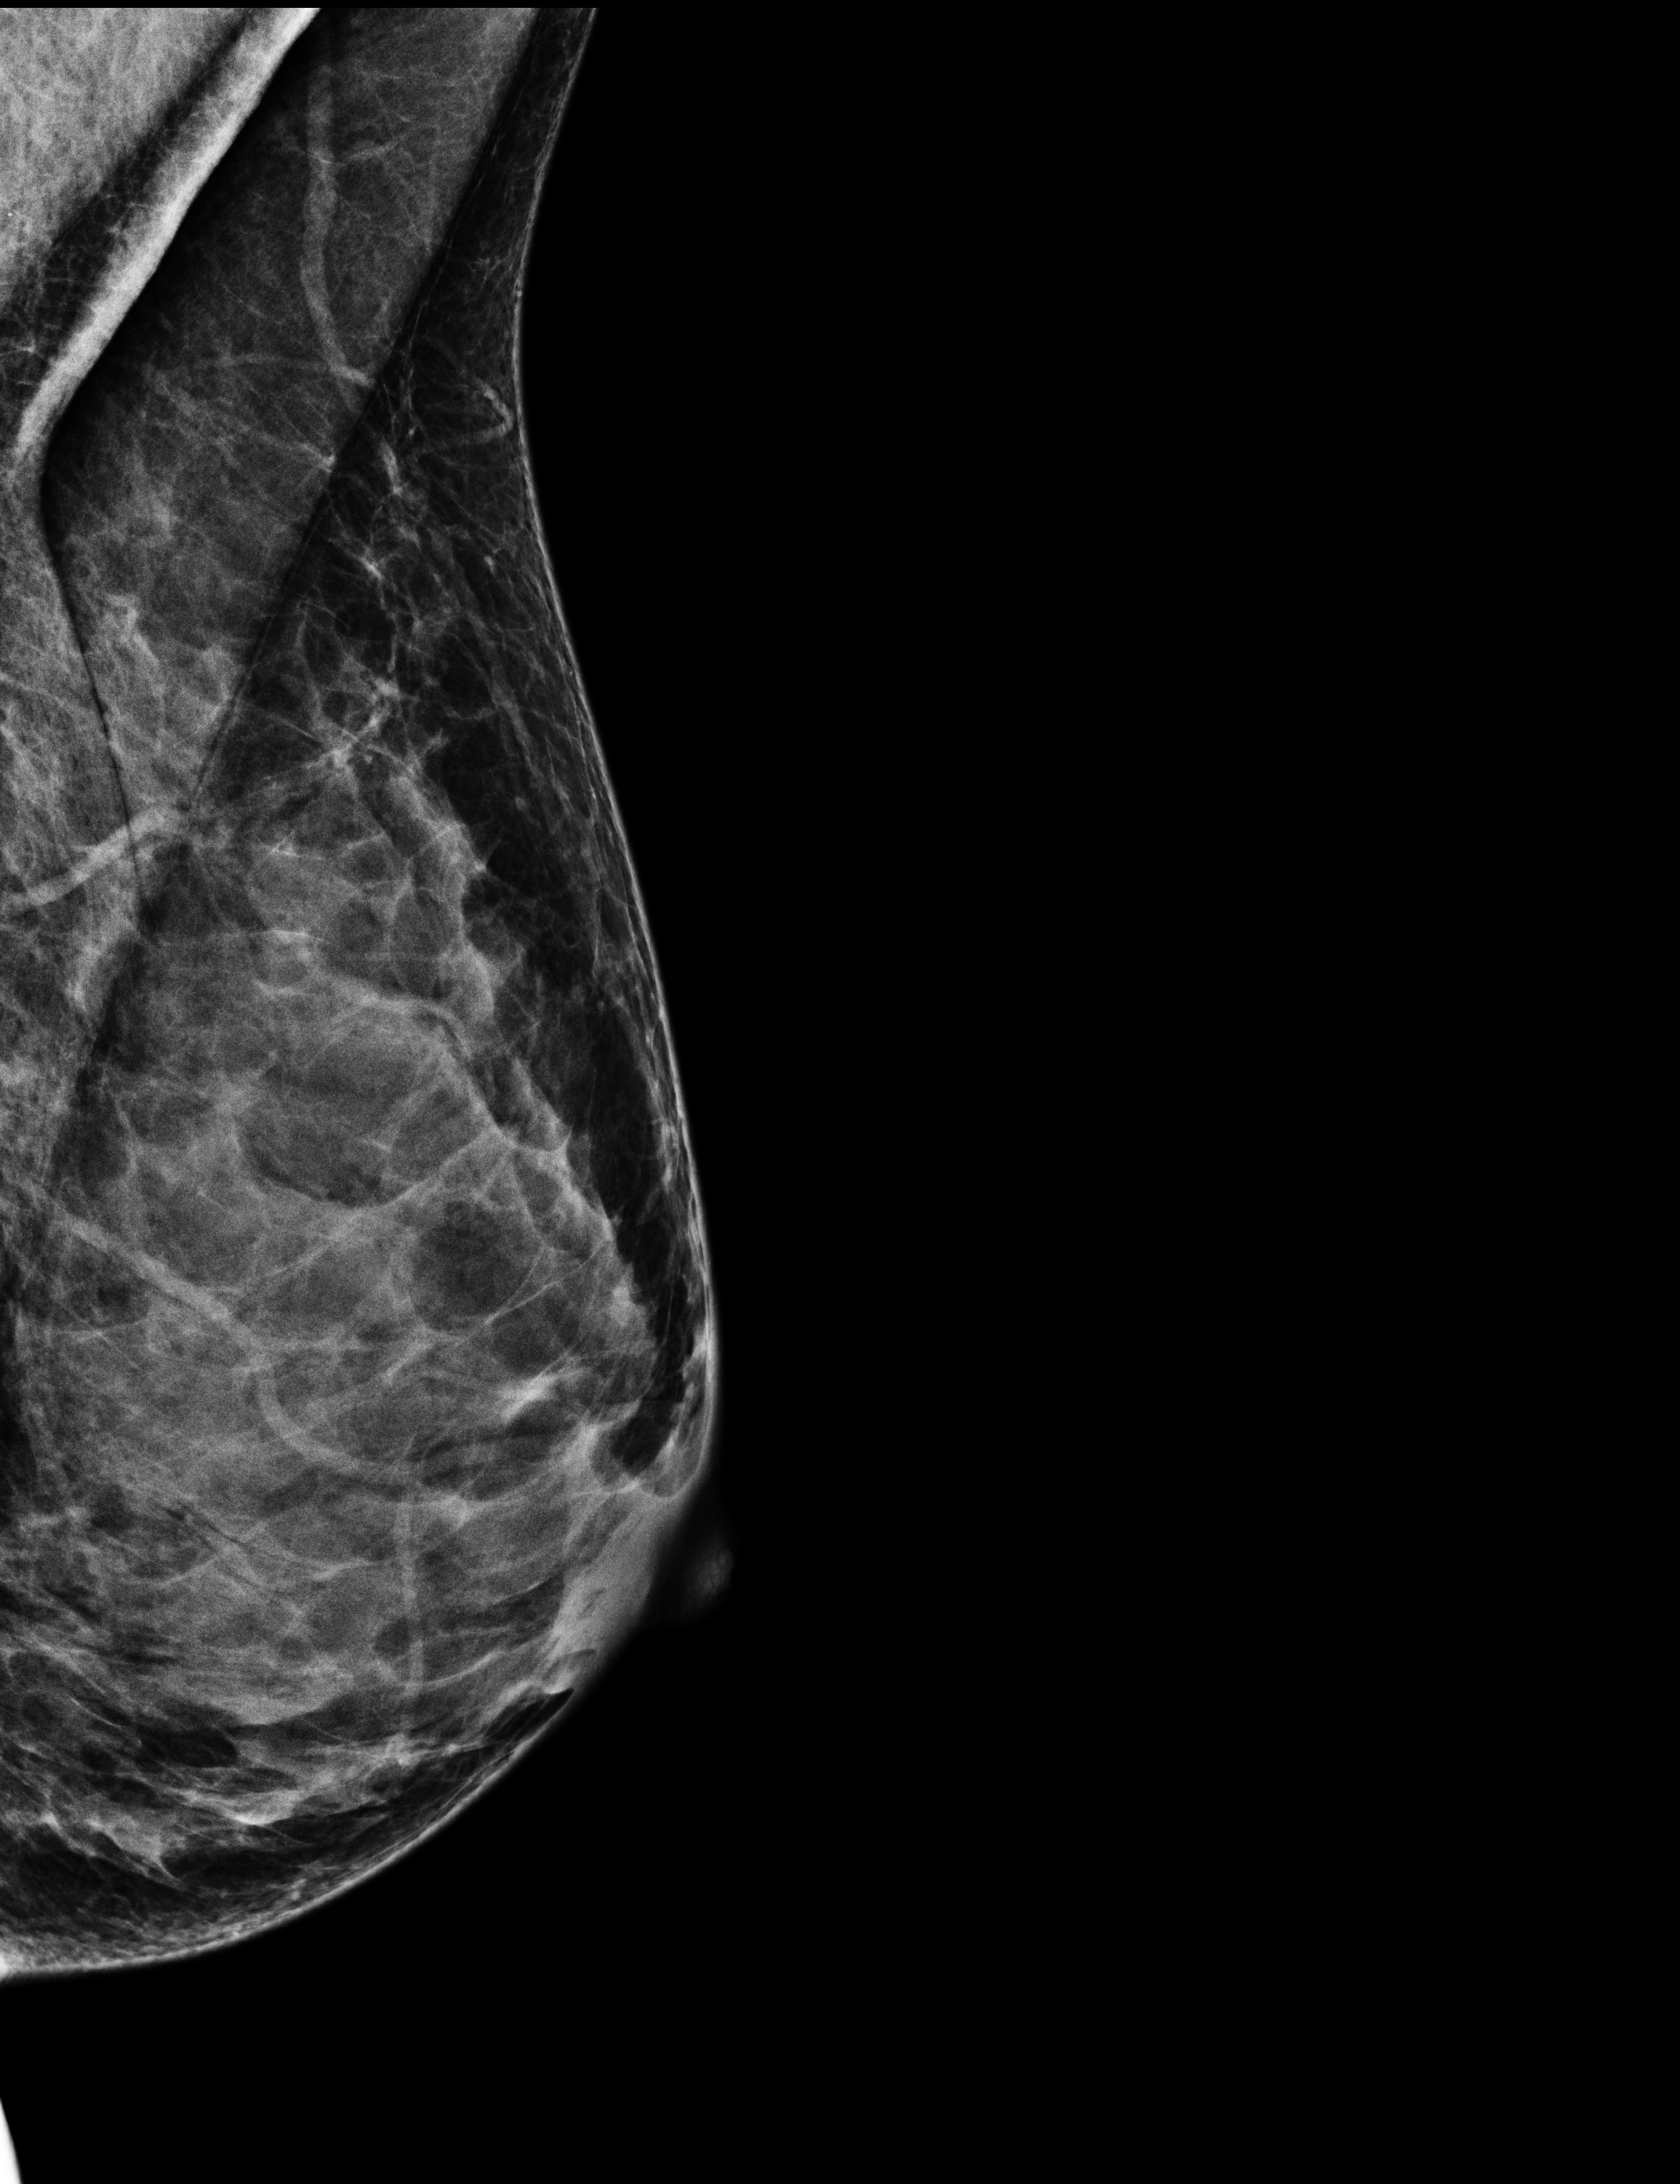
Screening examination, compressed breast thickness 40 mm. Female patient, age 43 years.
Image type: full-field digital mammogram. Breast: left. Projection: medio-lateral oblique projection.